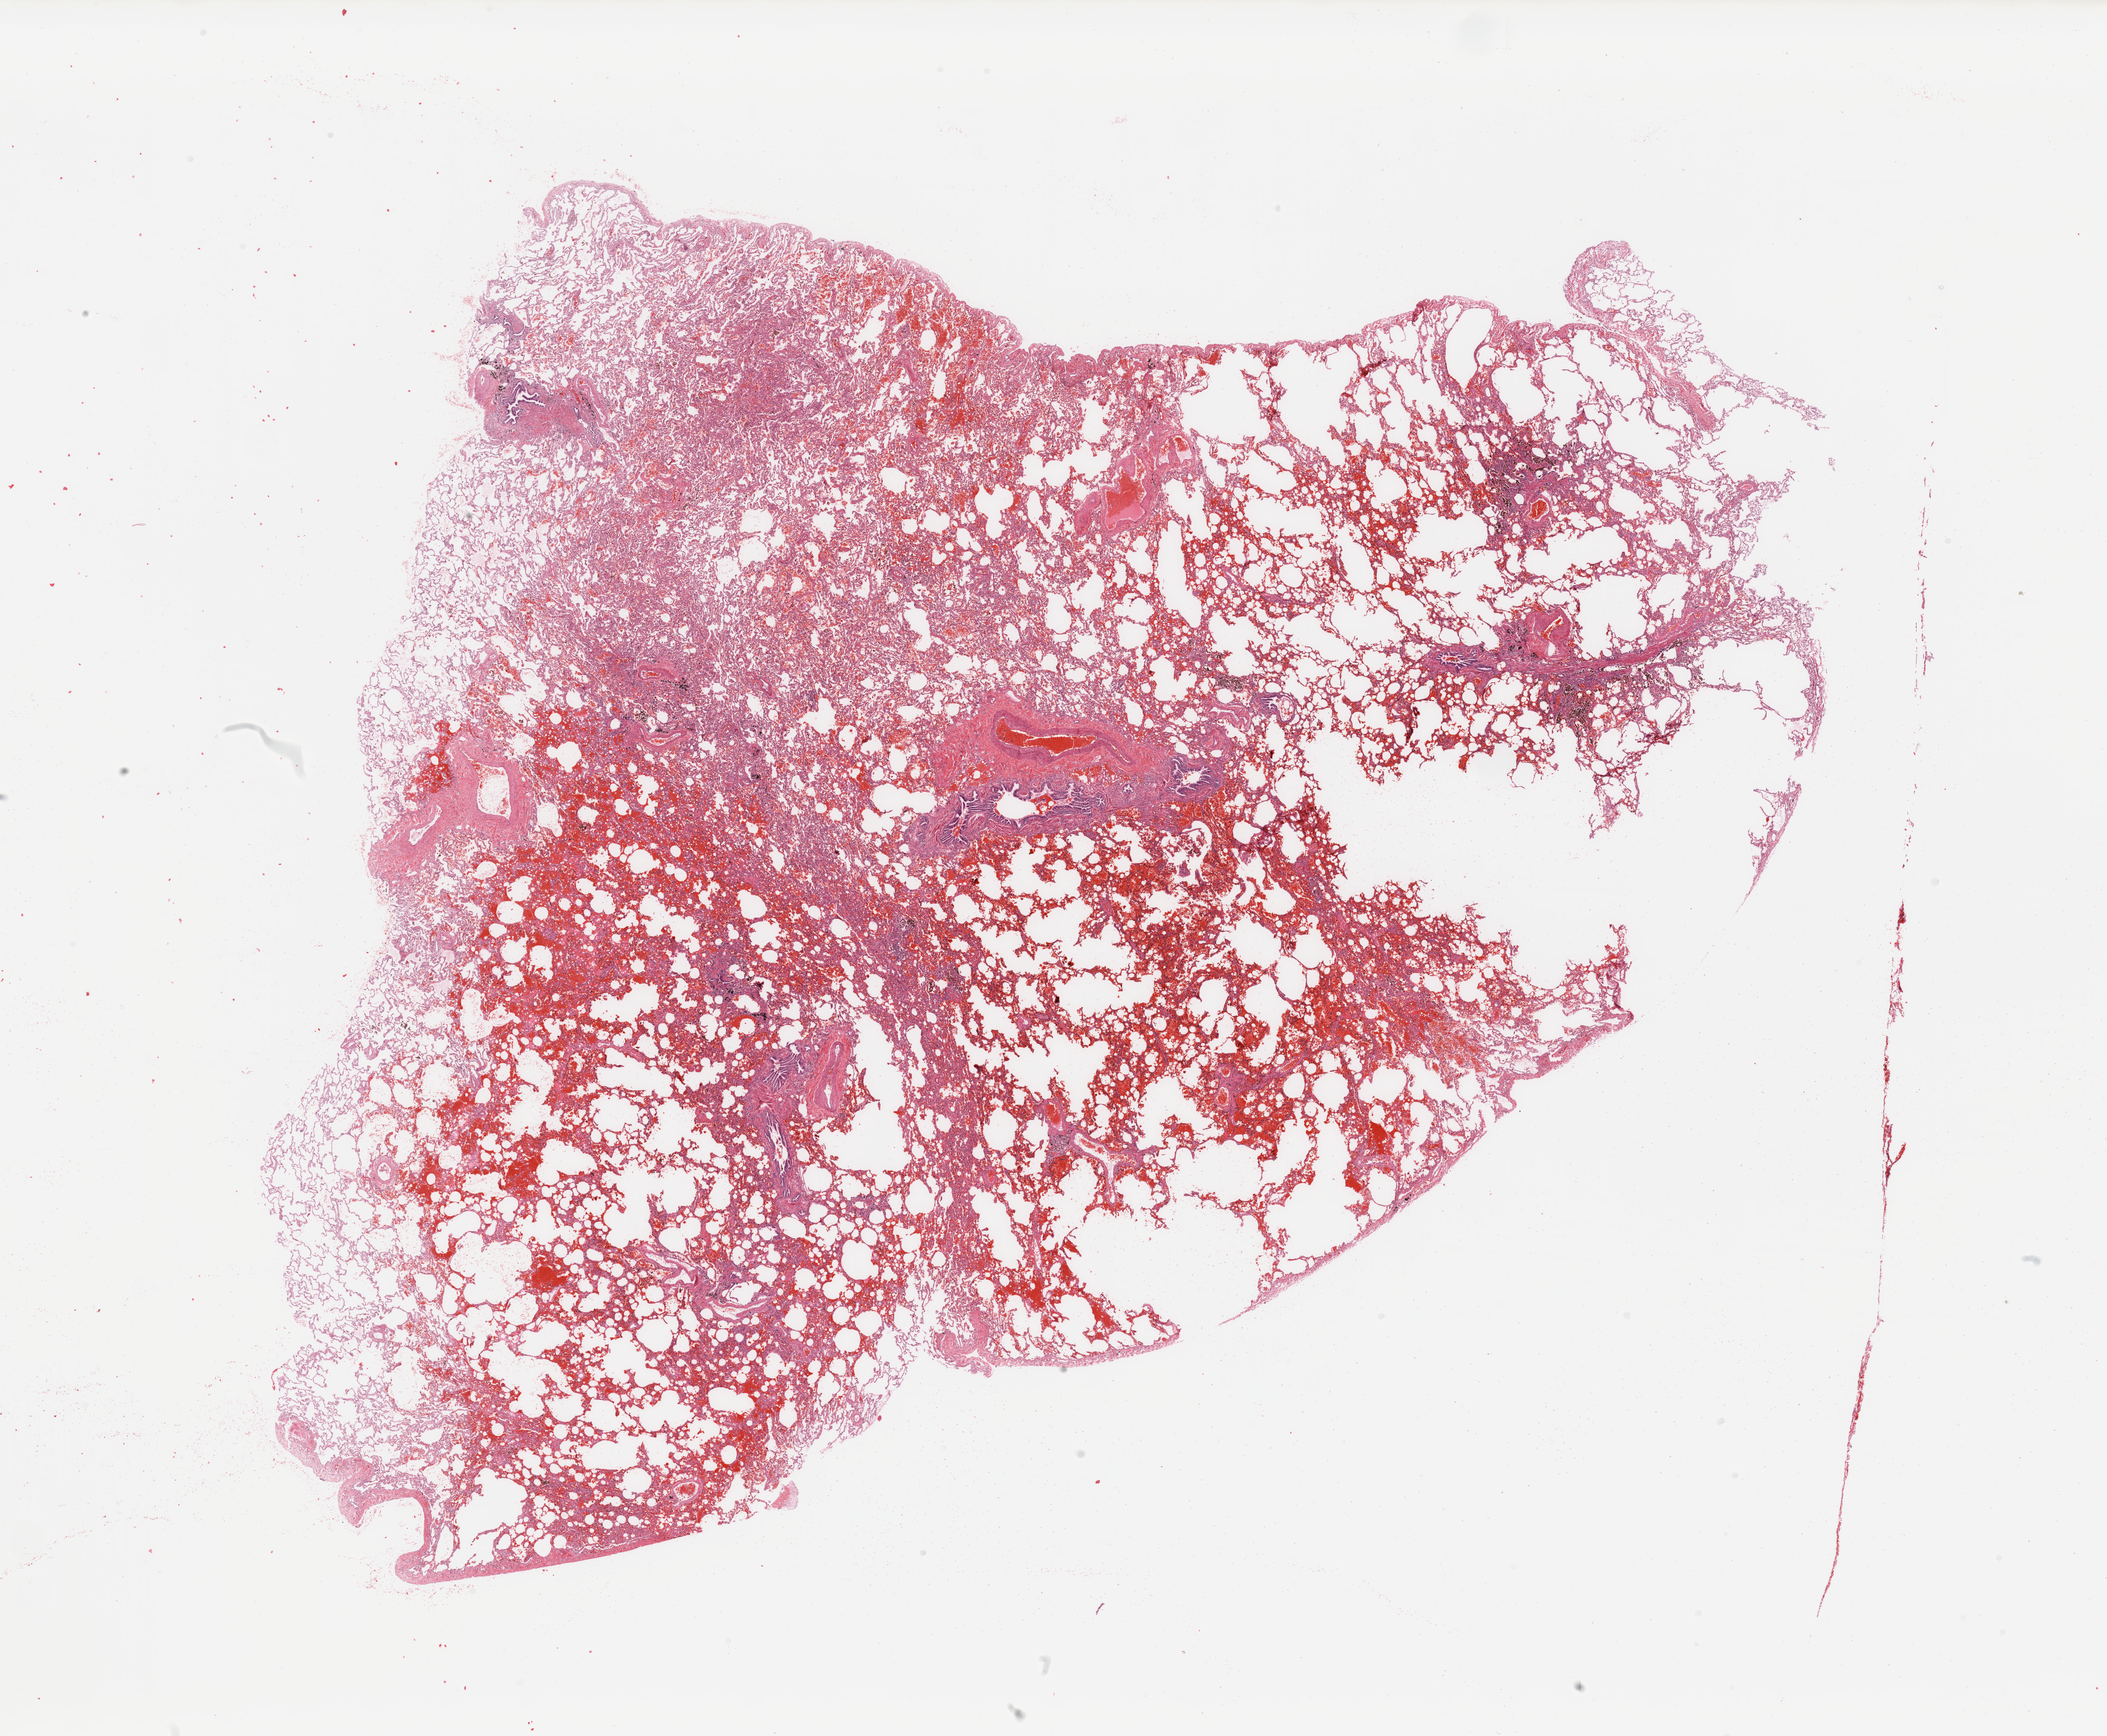
Hematoxylin and eosin (H&E) stained whole-slide image, shown as a low-resolution overview of the whole scanned area (about 27.6 x 22.7 mm, from a 20x scan), normal (non-tumour) tissue sample, sampled site: lung. Male, 60 y/o.
- this section: normal (non-tumour) tissue from the same patient
- patient diagnosis: Adenocarcinoma, NOS